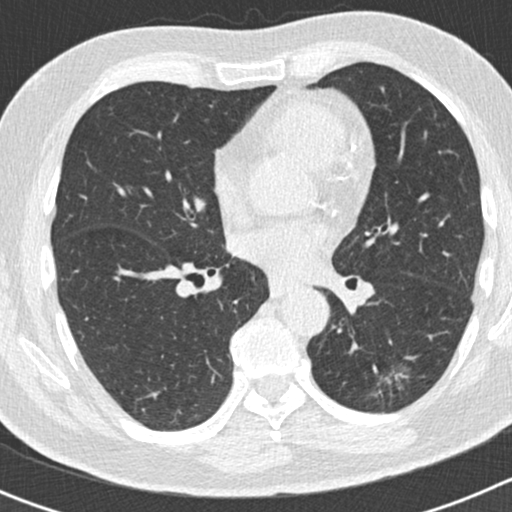
Chest CT (low-dose screening protocol), one axial image, second annual screen, lung window (W 1500 / L -600 HU), 2 mm slice thickness, slice 86 of 186 in the series. Male, age 66 years at enrolment. Former smoker at enrolment.
Lesion marked by an expert reader, bounding box [x1, y1, x2, y2] px = [352, 341, 410, 408]. Reader record for this screening exam (exam-level; its link to the box is not recorded): non-calcified nodule or mass ≥4 mm, left lower lobe, 50 × 33 mm, smooth margins, pre-existing on the prior screen: yes; interval growth: yes. Later outcome: lung cancer diagnosed 440 days after this screen (after the third annual screen) — adenocarcinoma, NOS, left lower lobe, poorly differentiated (G3), stage IB (AJCC 6th edition), 38 mm at pathology.